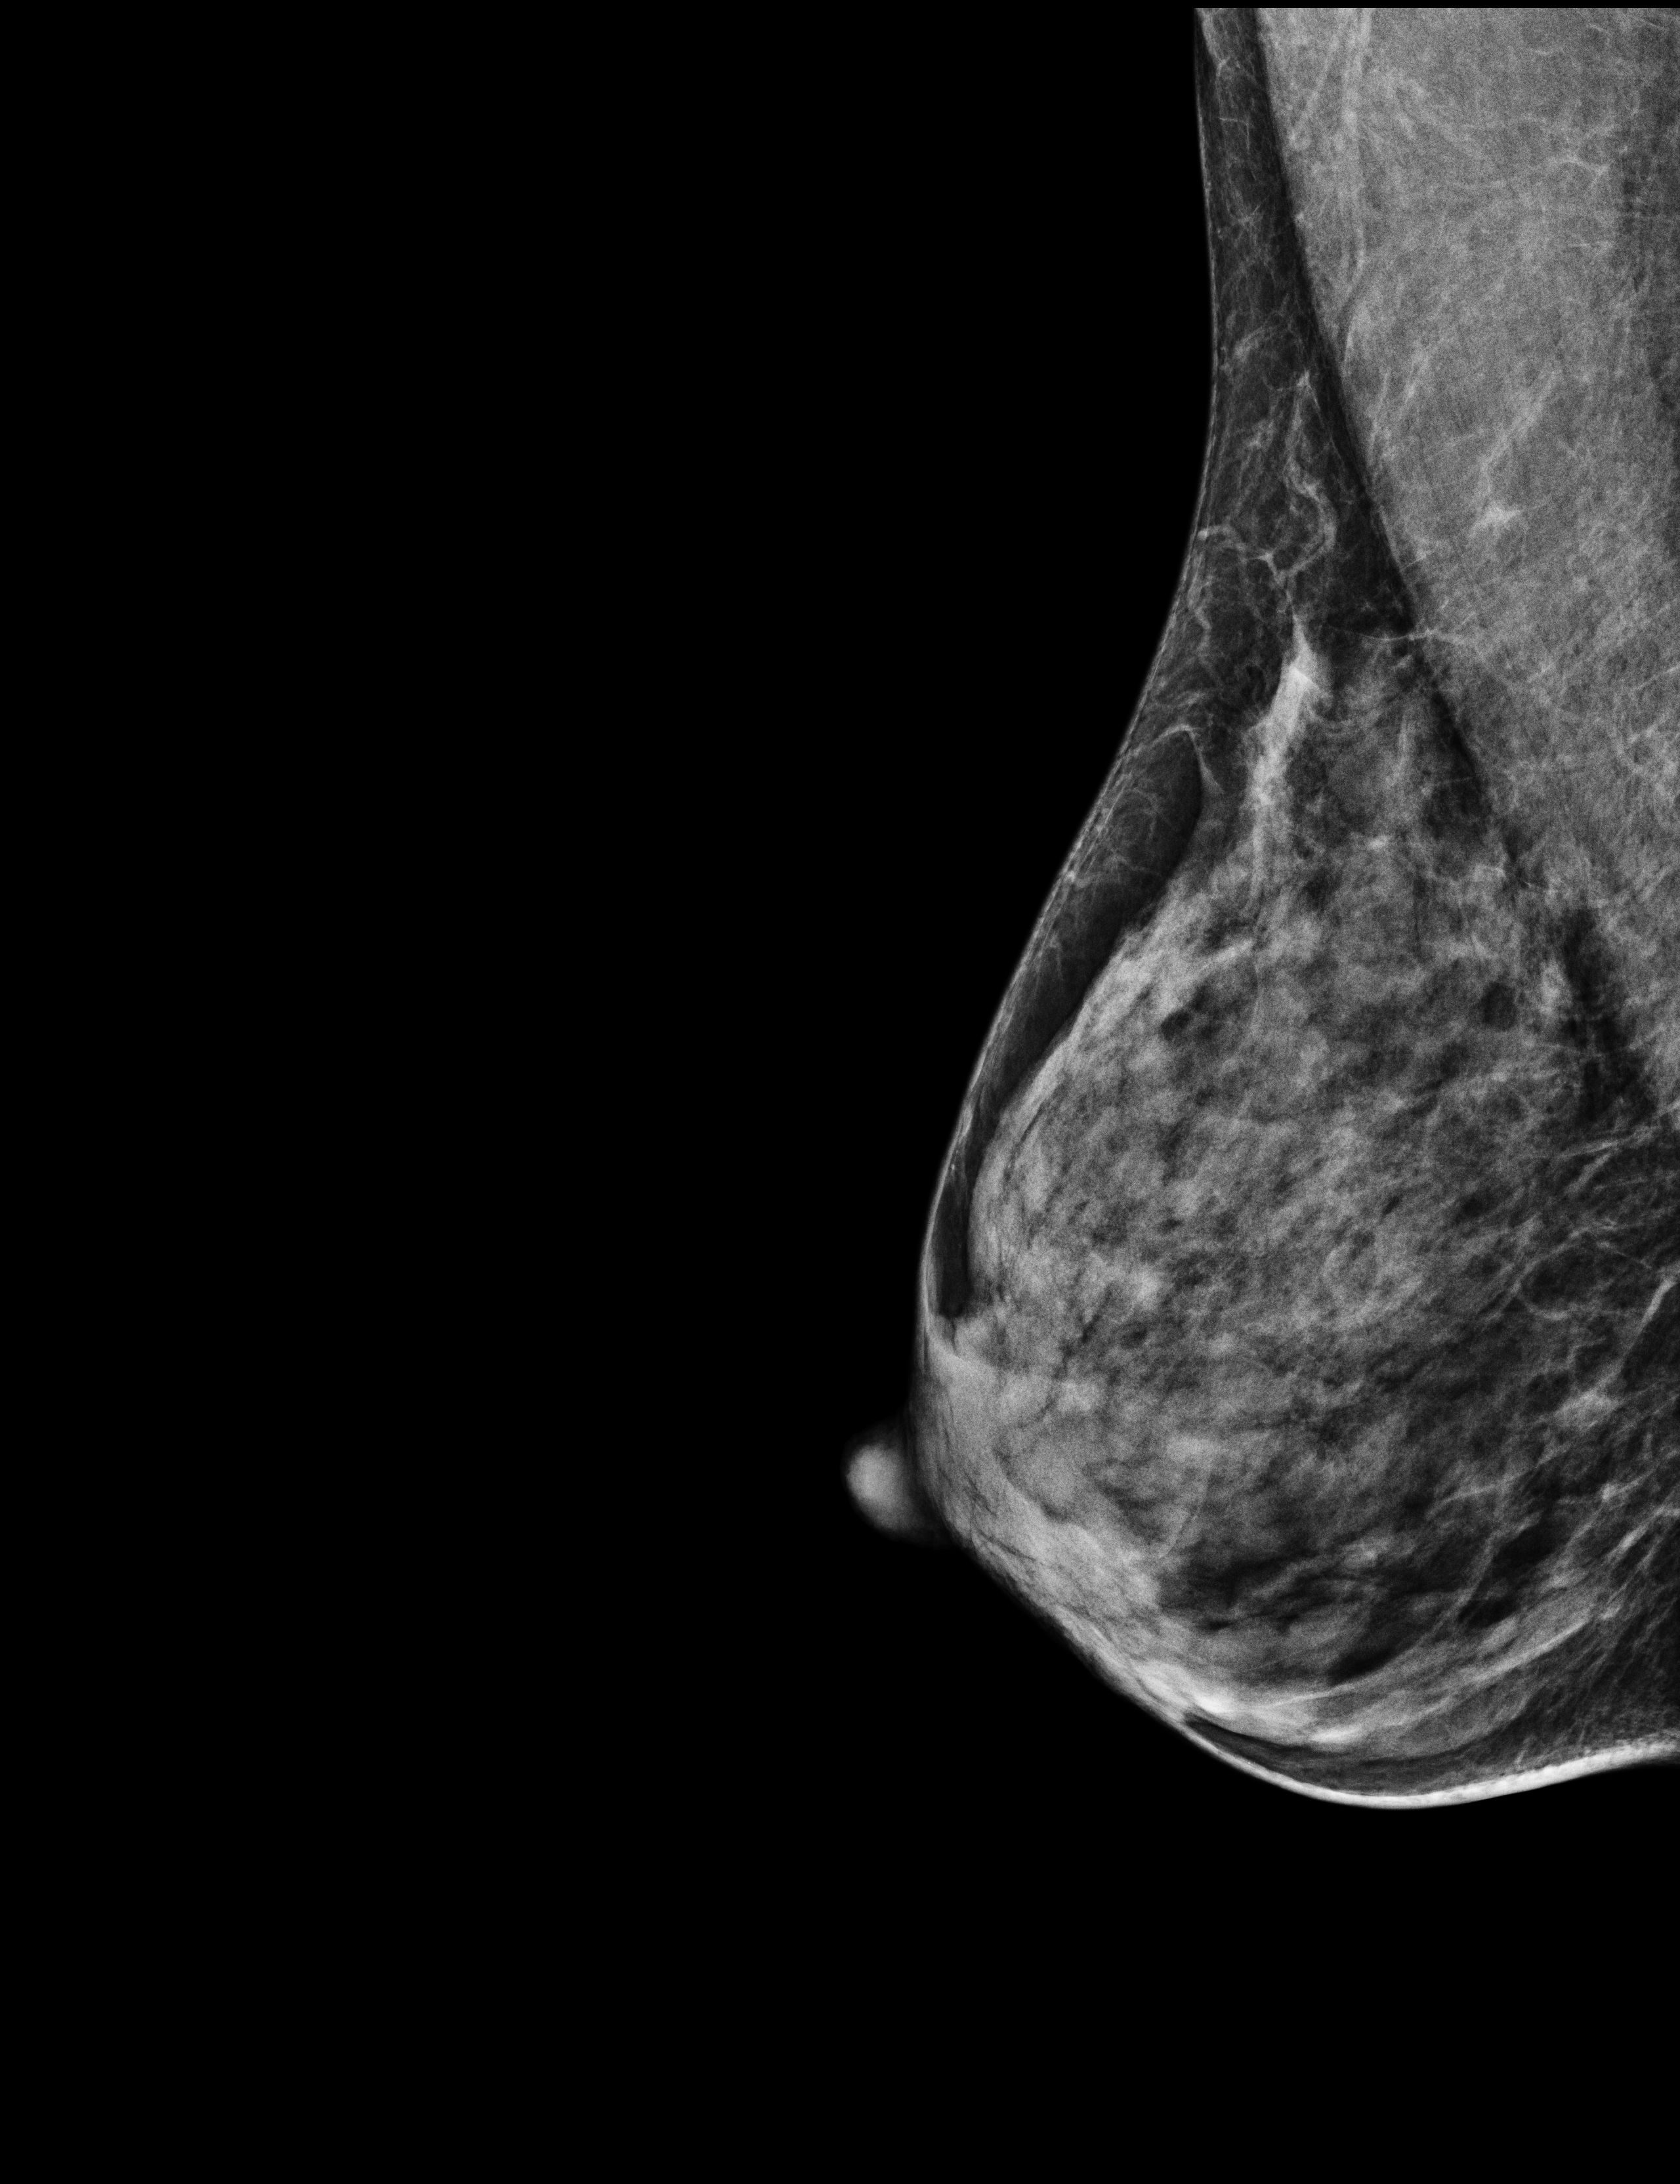
Digital mammogram (FFDM), right breast, mediolateral oblique (MLO) view, annual screening mammography examination. Female patient, age 55 years.
BI-RADS breast density category at the screening exam (both breasts, scale 1–4): 3. Final BI-RADS category for the screening round (tomosynthesis exam, both breasts): category 2. Recall: no recall after this screen.